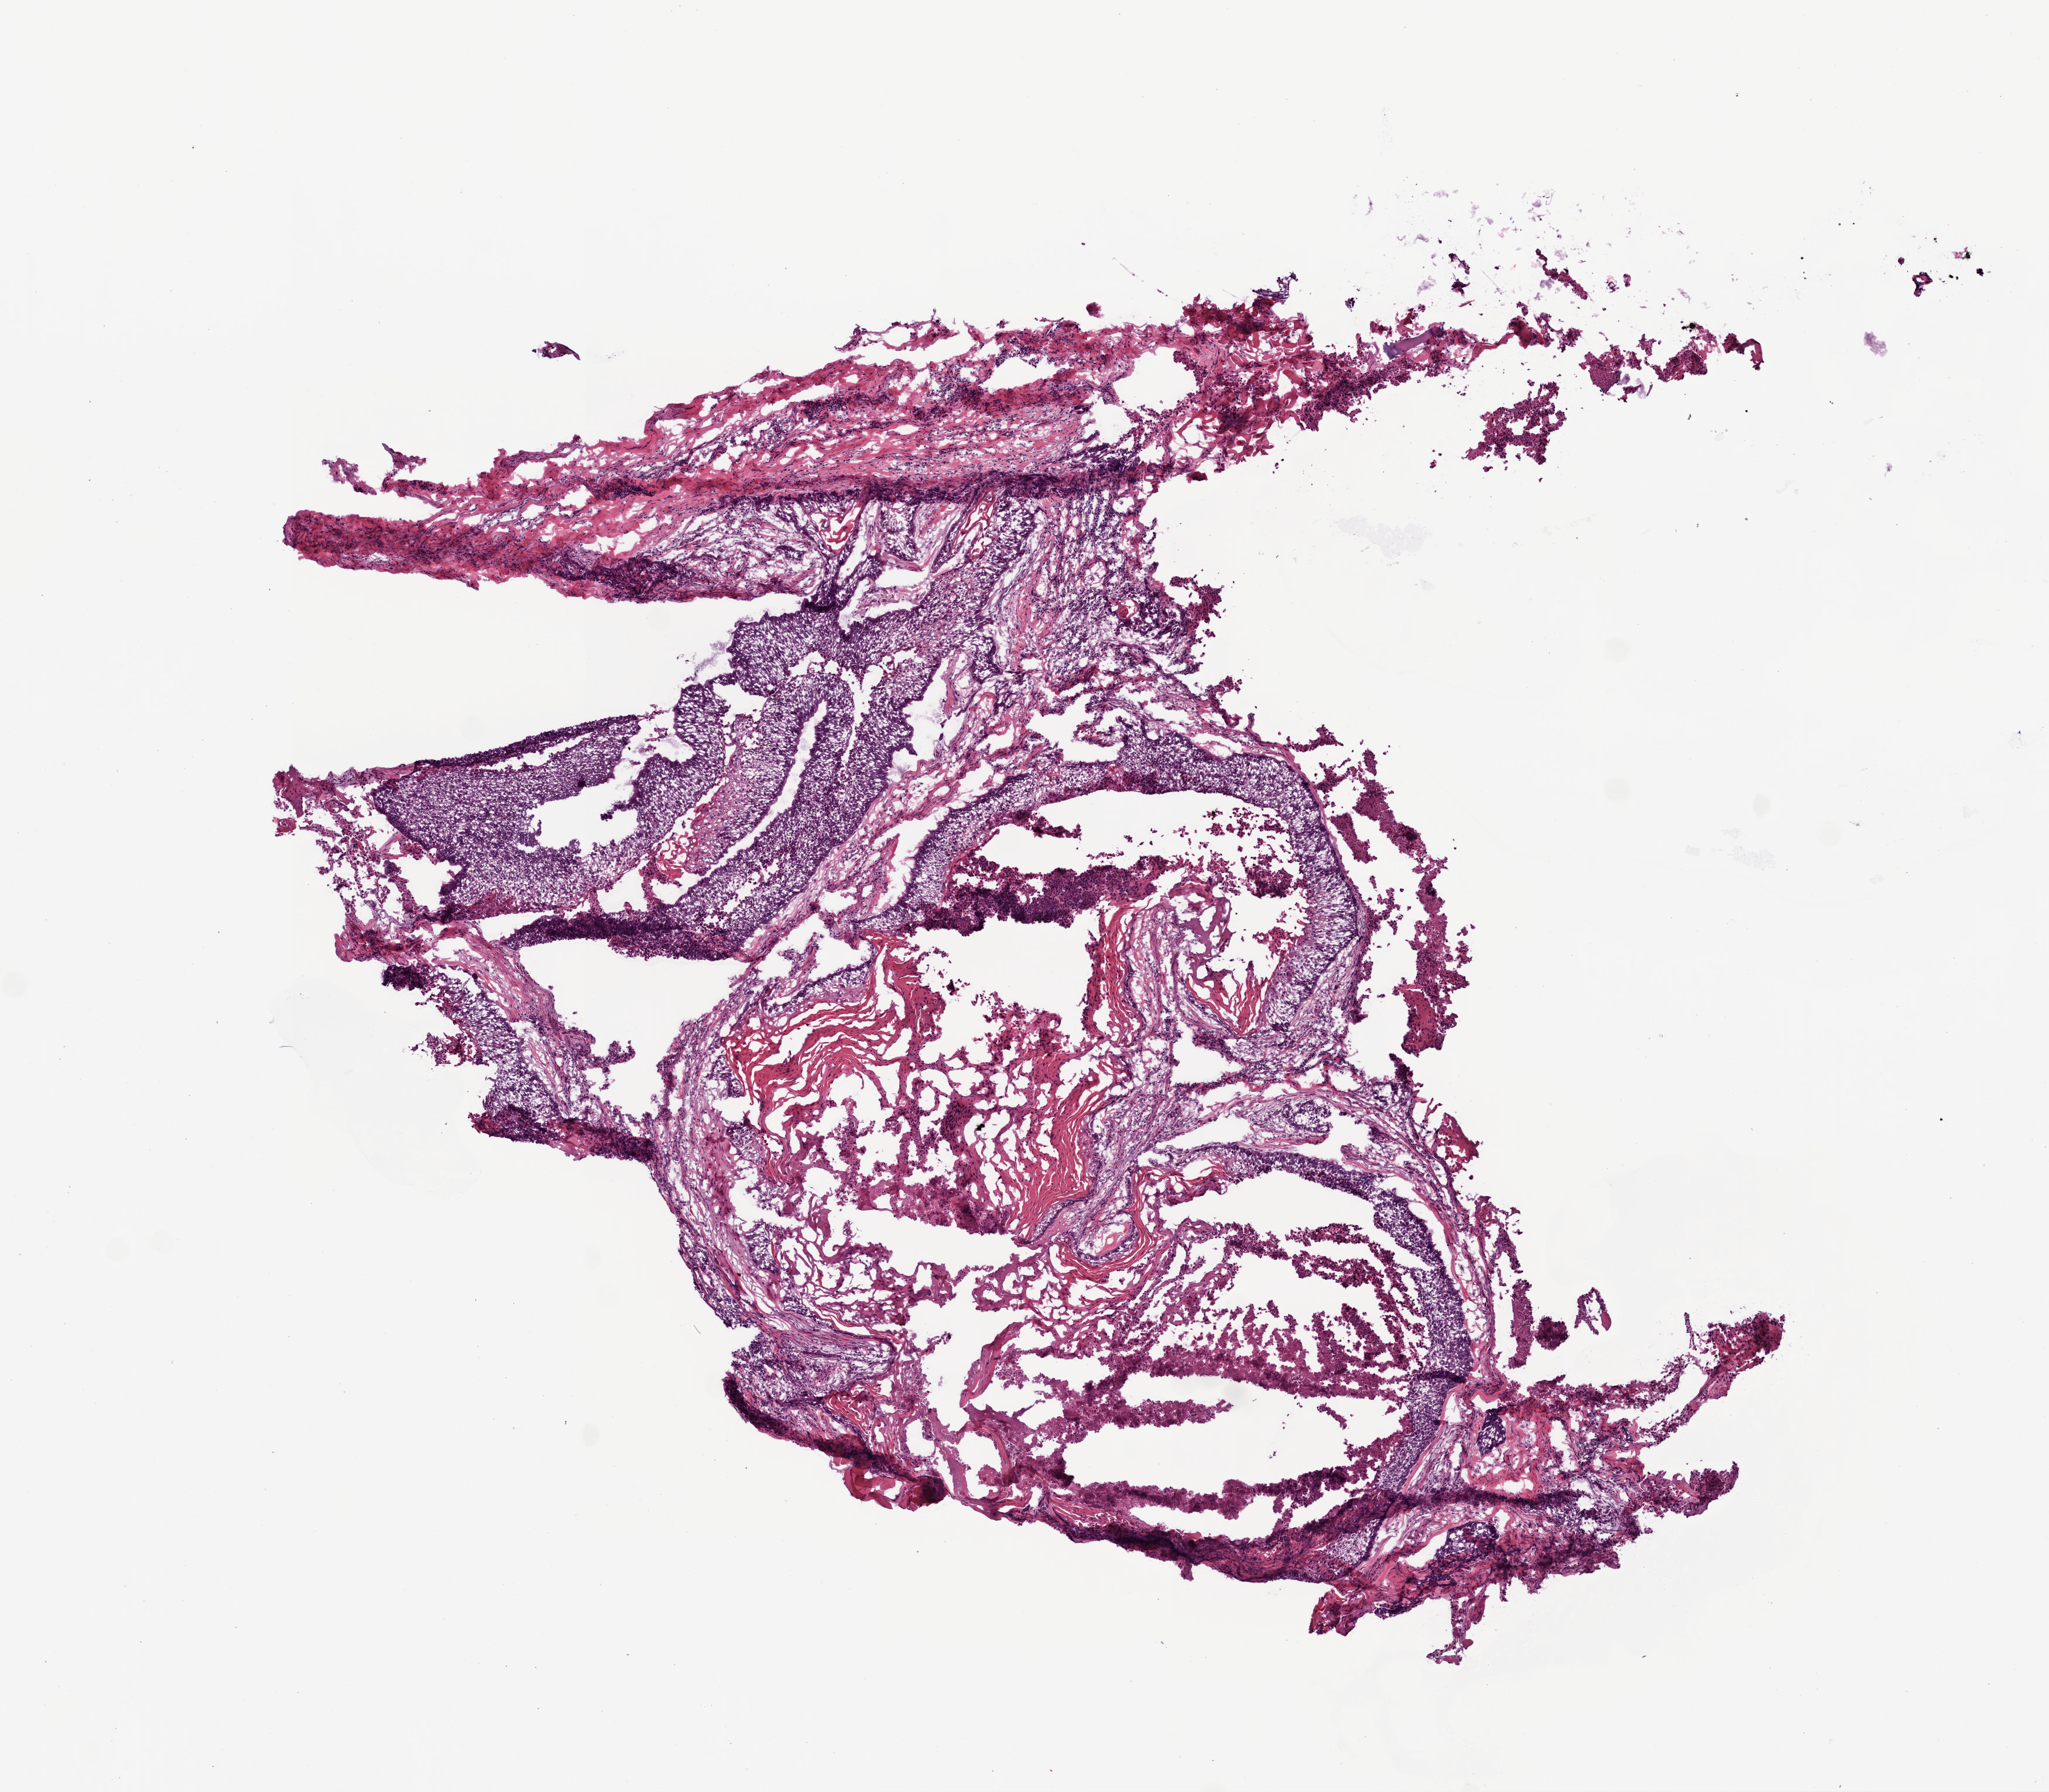
Whole-slide histology image, Hematoxylin and eosin (H&E) stained, a low-resolution overview of the entire scanned area, about 7.0 x 6.1 mm (from a 20x scan). Frozen section from the top of the tissue portion. Head and neck, primary tumour sample. Male patient; age at initial diagnosis 60 years. Pathologist review of this section (percent, as recorded): tumour cells 60%, tumour nuclei 70%.
Histologic diagnosis: Squamous cell carcinoma, NOS (larynx, NOS).